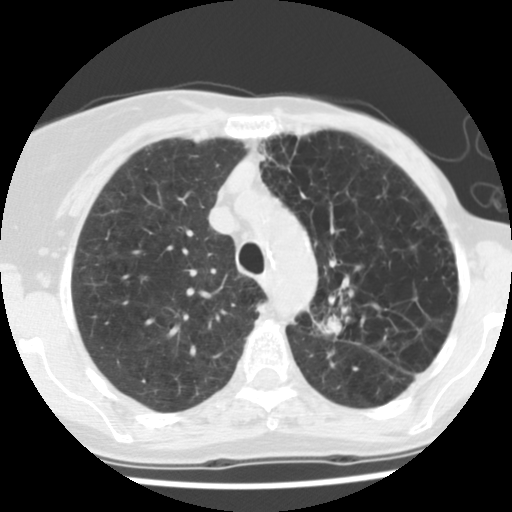
Low-dose screening chest CT, one axial slice. Slice 95 of 128 in the series (ordered by position). 140 kVp. Lung window (W 1500 / L -600 HU). 512 × 512 image matrix, field of view 290 × 290 mm.
Annotated regions visible in this slice (expert manual segmentation):
- lesion 1 (tumor, upper lobe of left lung): bounding box [x1, y1, x2, y2] px = [317, 315, 342, 335]